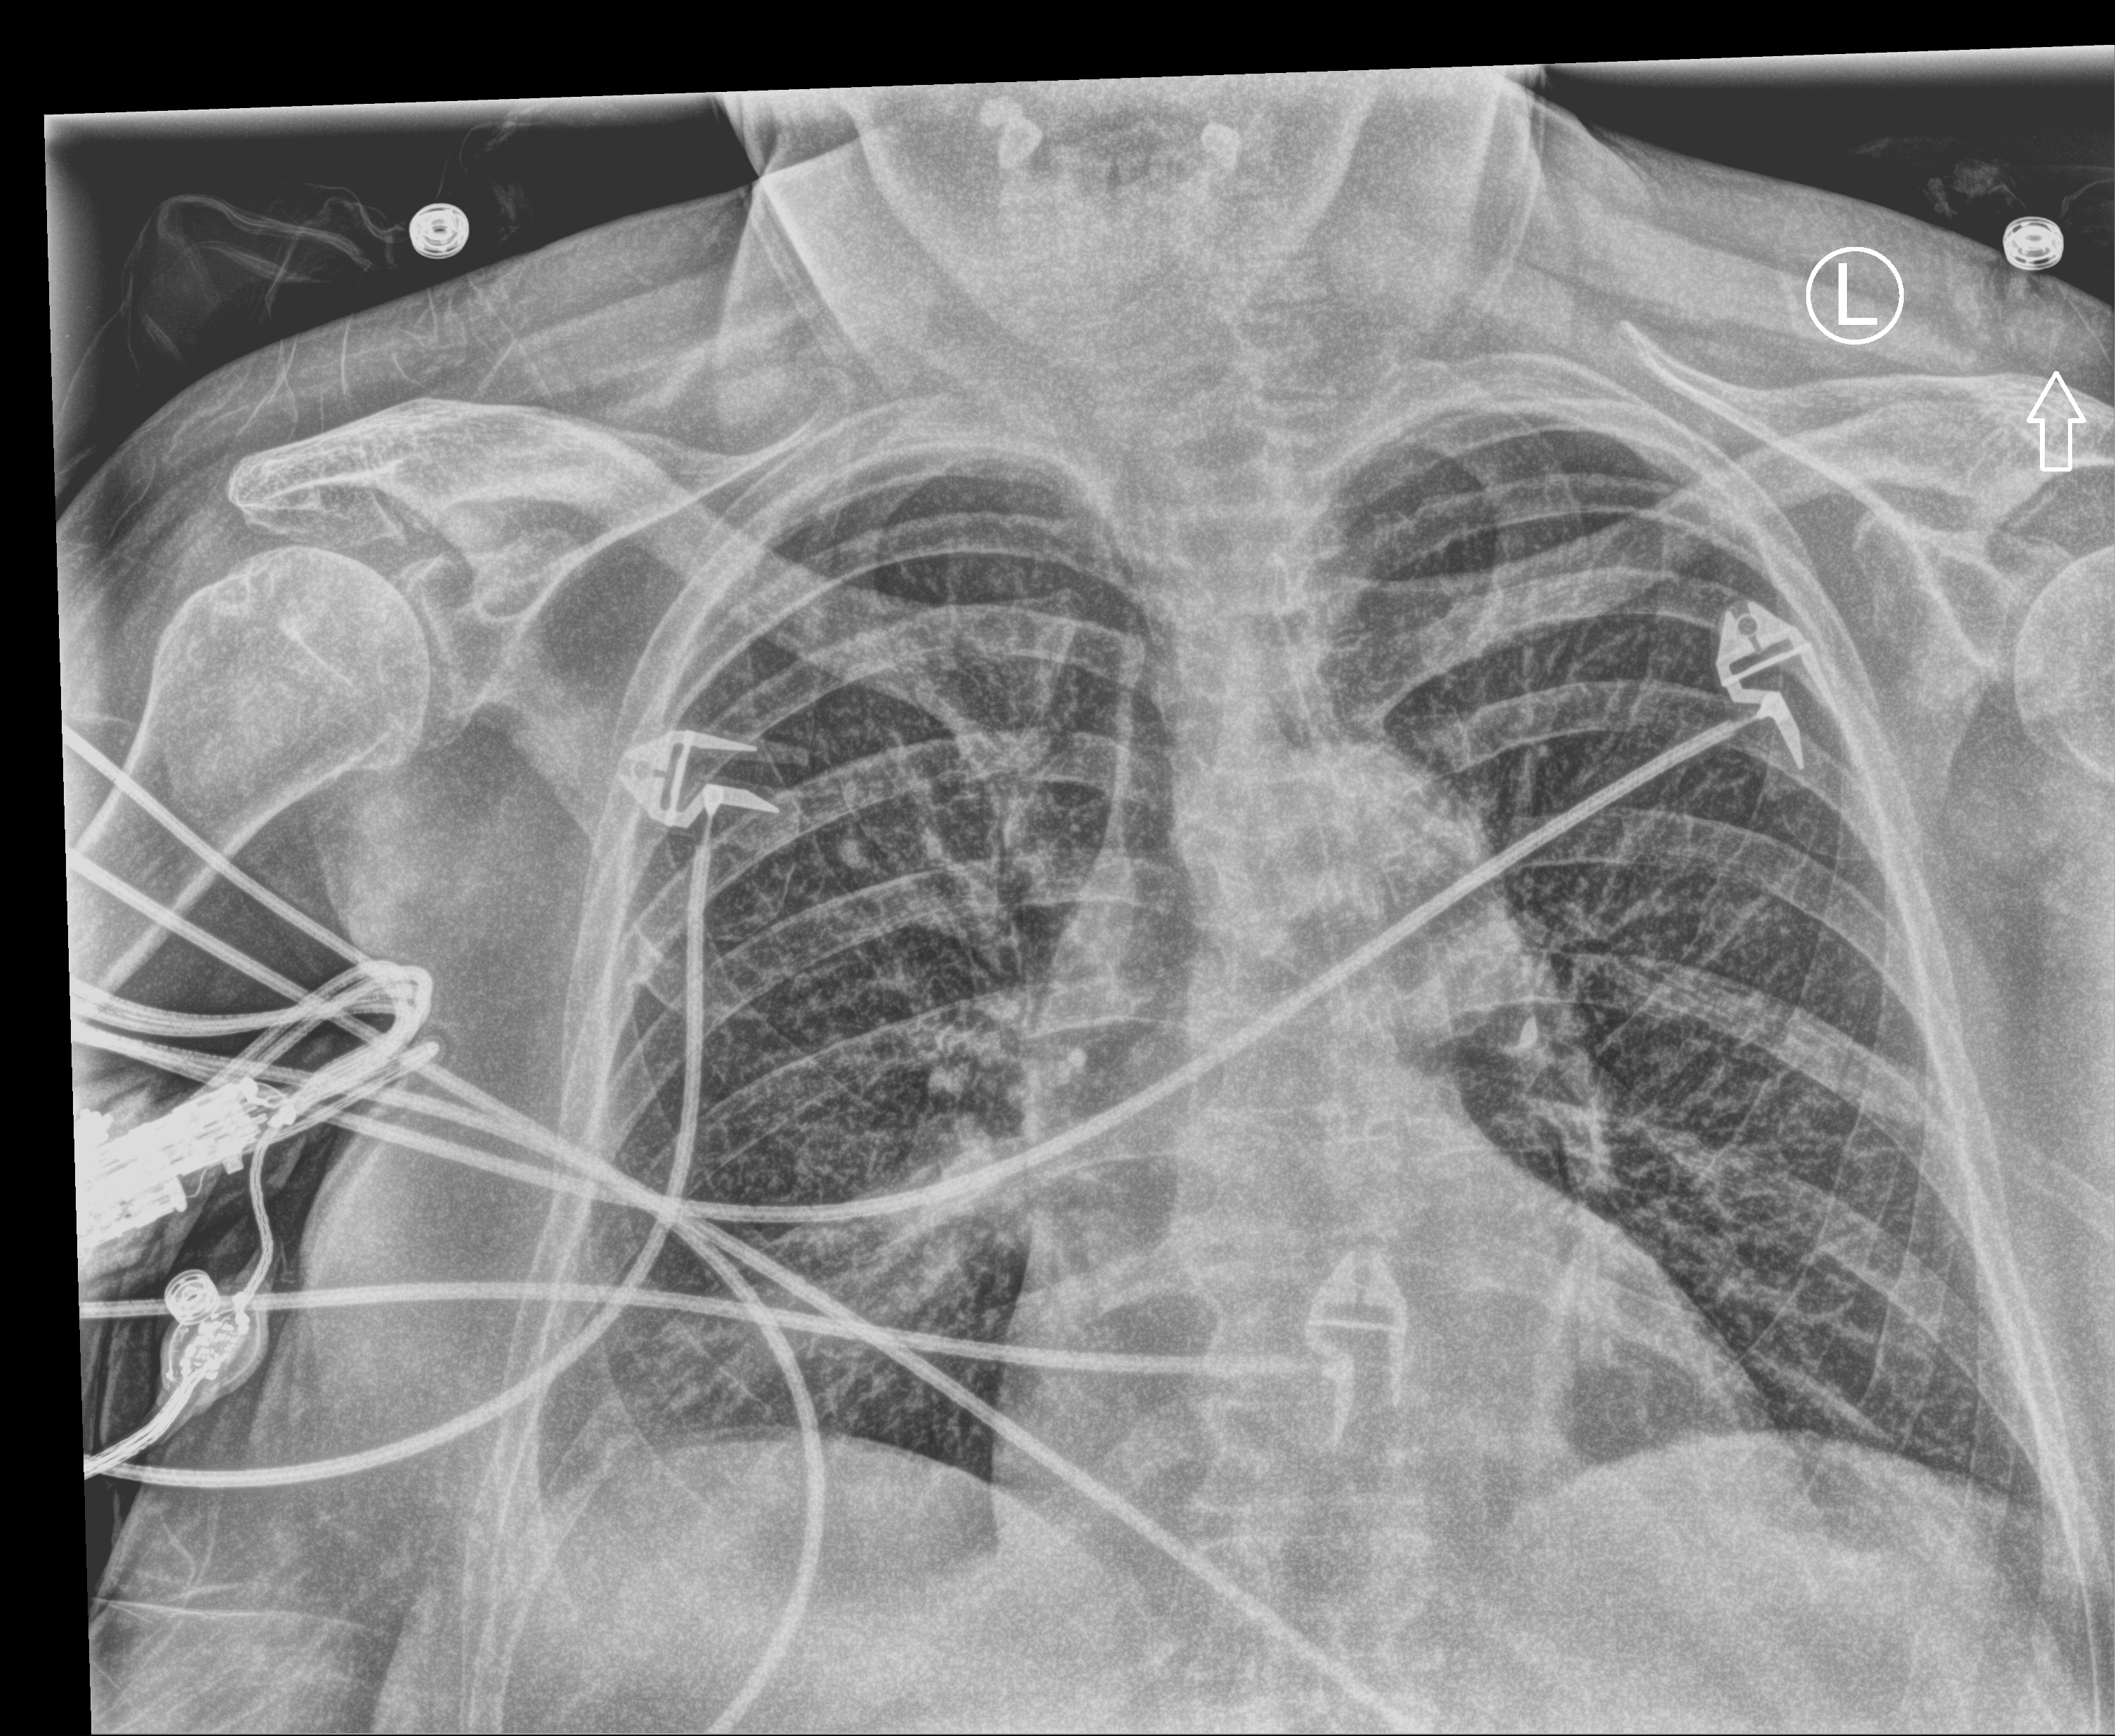
Chest X-ray (portable), anteroposterior (AP) projection. Female patient hospitalised with COVID-19, age 75–90 years.
From the hospital-stay record, not from the radiograph (when in the stay this image was taken is not recorded):
- admitted to intensive care during this hospital stay: no
- mechanically ventilated during this hospital stay: no